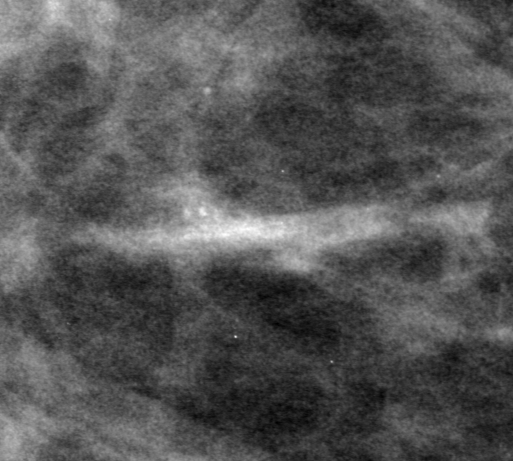
Cropped region of a digitized screen-film mammogram centred on a radiologist-marked abnormality; right breast; CC view.
- Finding: calcifications, morphology punctate, distribution clustered; BI-RADS assessment category 0; pathology (as recorded): benign.